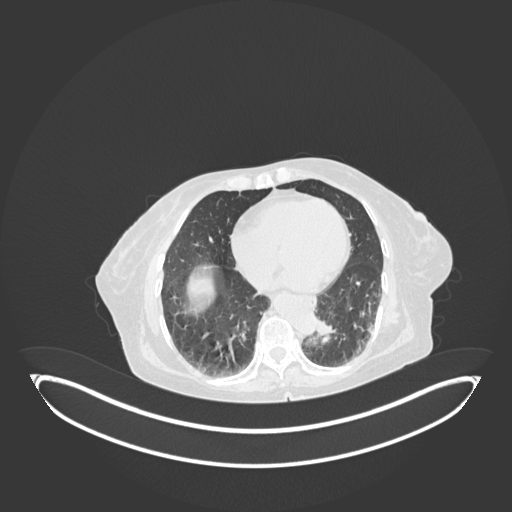
Chest CT, one axial slice; position 25 of 189 along the scan axis; 120 kVp; lung window (W 1500 / L -600 HU); 1 mm slice thickness; 512 × 512 image matrix. Patient: female, 82 years. From the clinical record (not read from this slice): clinical TNM (as recorded): T1b N0 M1.
Annotated regions visible in this slice (rectangle marked by the reading radiologist):
- lung tumour (recorded histology: adenocarcinoma): bounding box <316,316,341,352> (left, top, right, bottom; pixels)